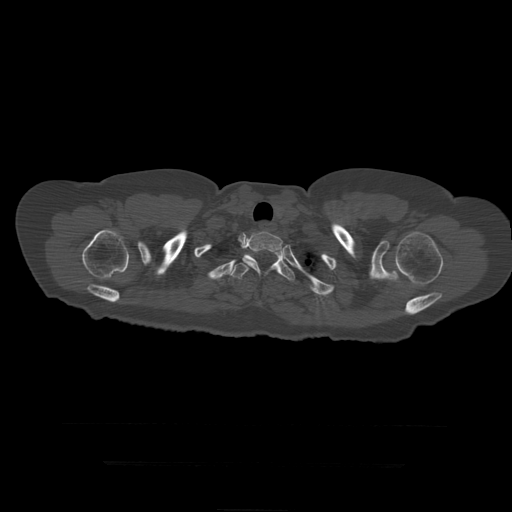
CT including the spine, one axial slice; reconstruction kernel STANDARD; bone window (W 1800 / L 400 HU); 1.25 mm slice thickness; 512 × 512 image matrix, field of view 450 × 450 mm. Patient age 41 years. From the clinical record (not read from this slice): primary cancer: breast.
Outlined on this slice (semi-automatically segmented with operator editing):
- T2 vertebra: bounding box [x1, y1, x2, y2] px = [242, 232, 284, 276]
- T3 vertebra: [230, 251, 295, 281]